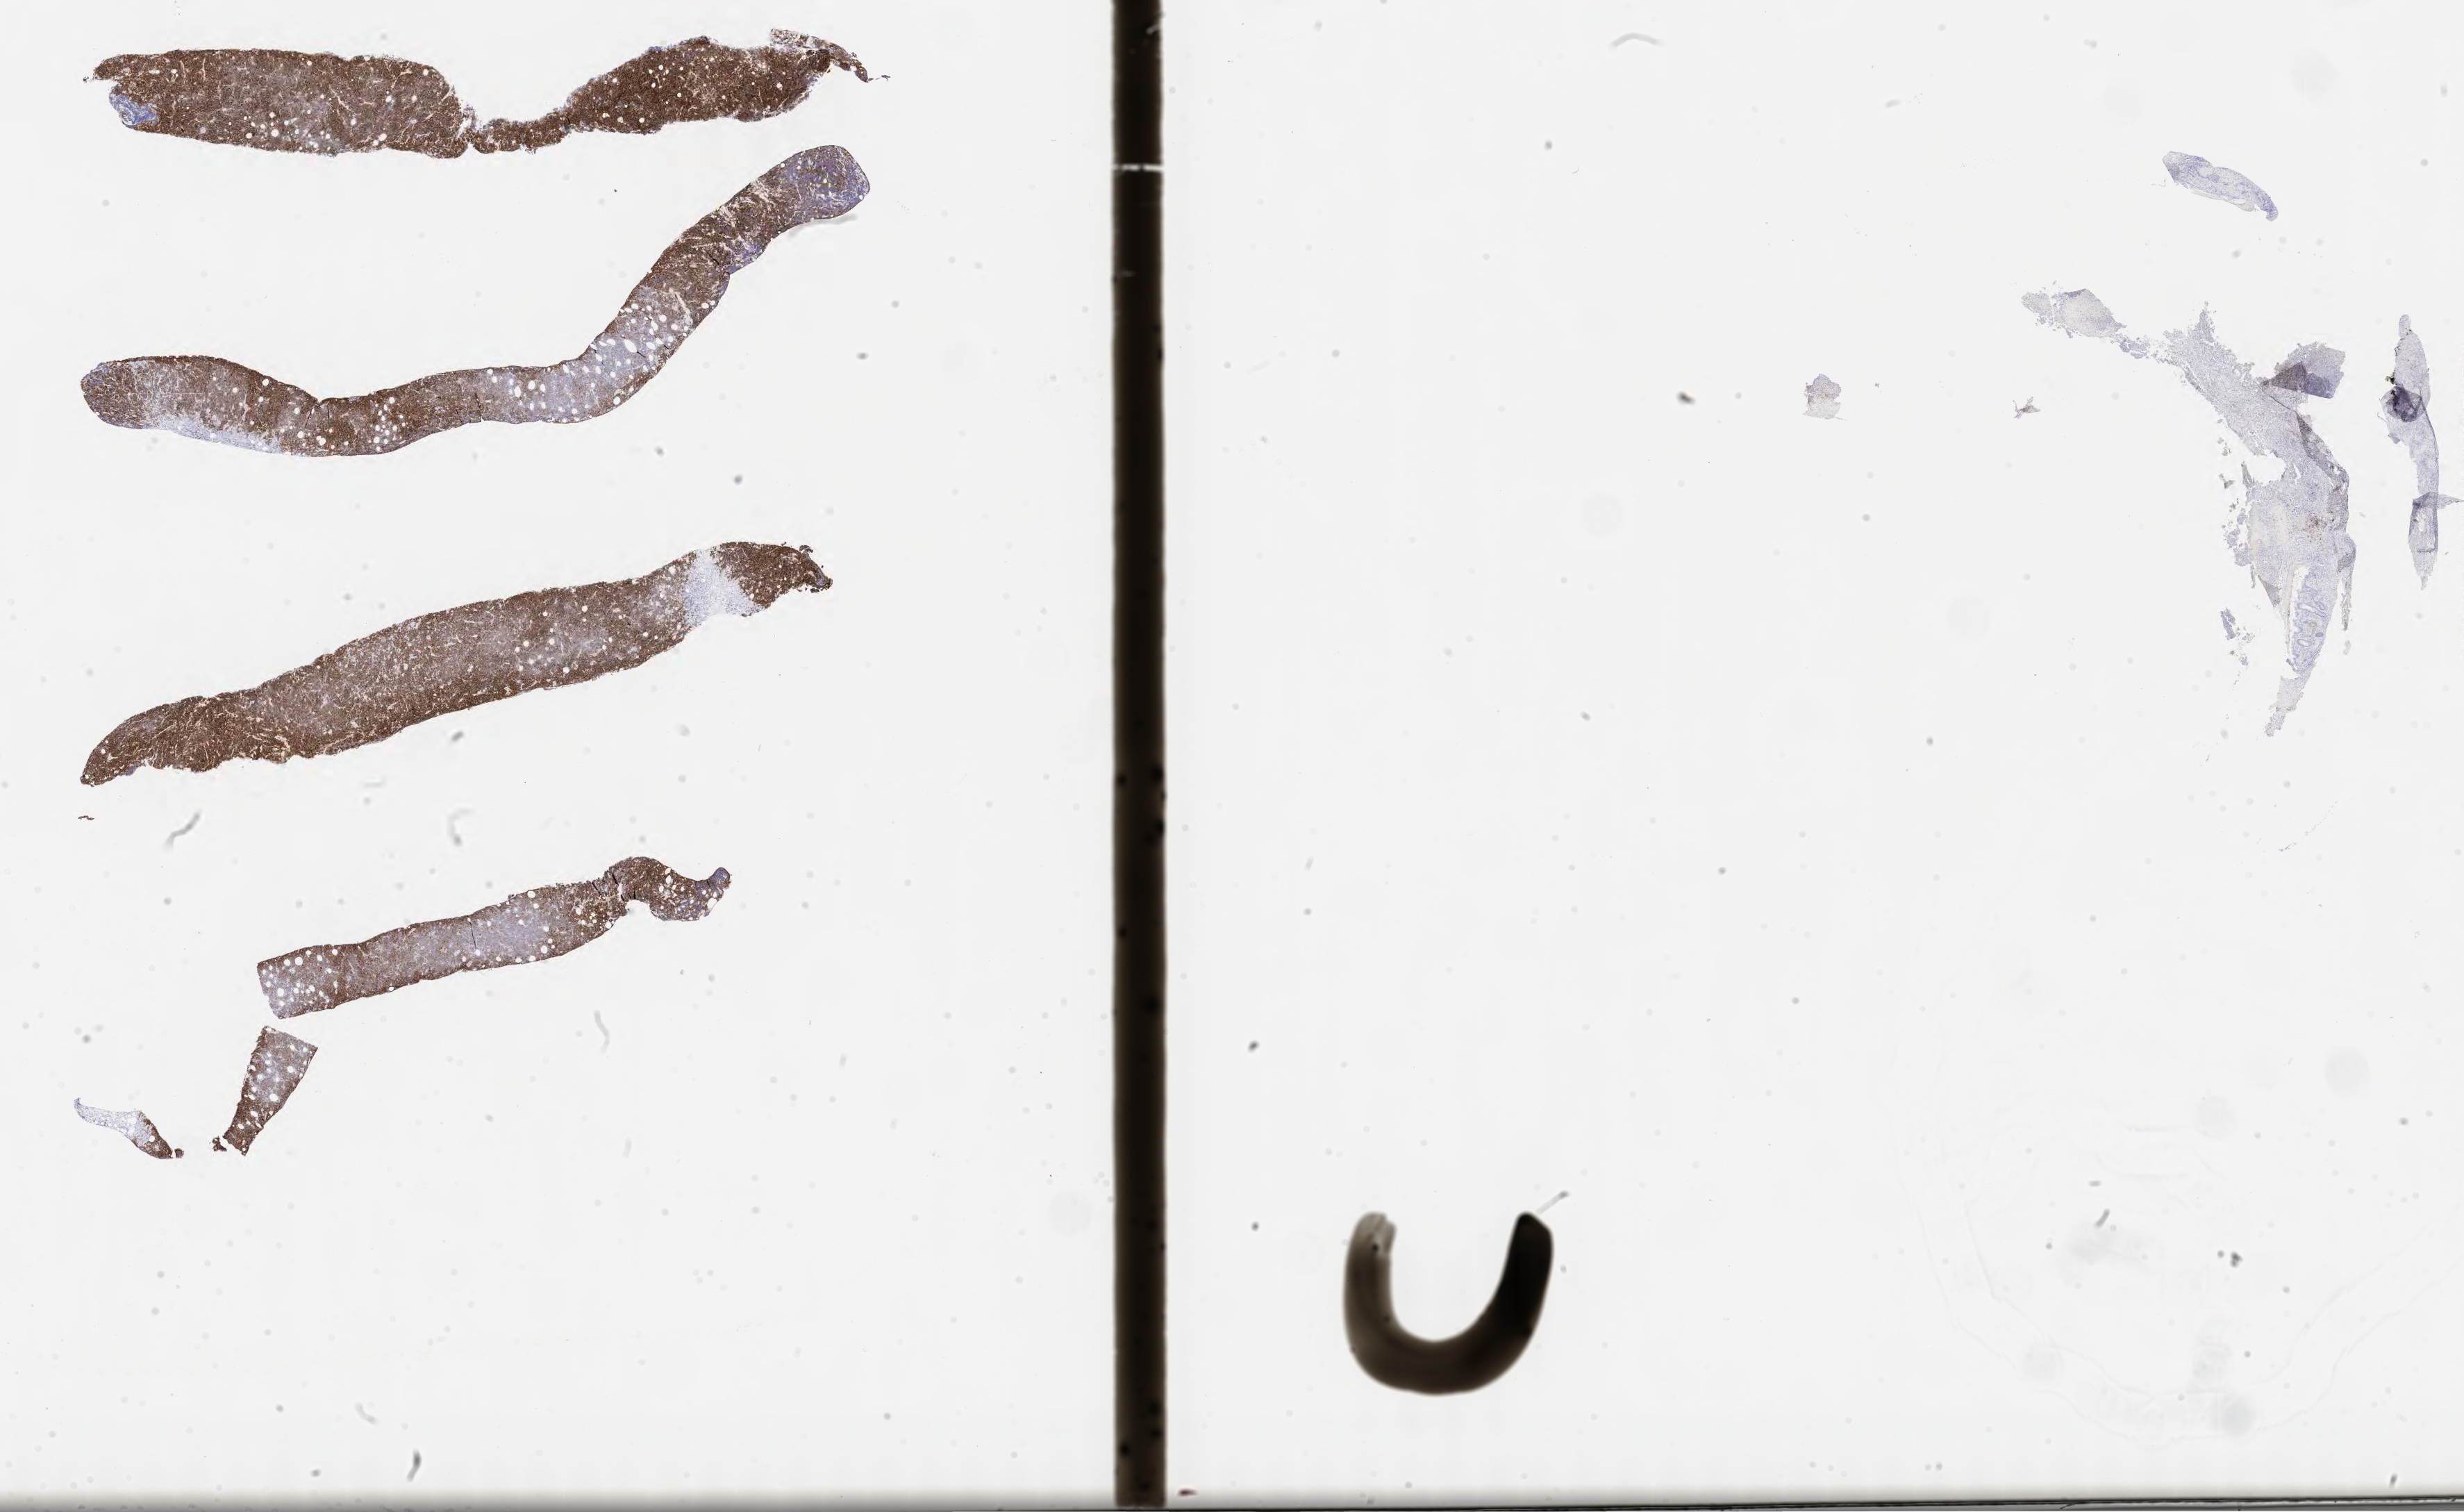
Whole-slide image, immunohistochemical stain for CD20 — whole scanned area (about 28.7 x 17.6 mm) shown as a low-resolution overview, specimen: tumor tissue. Male patient, 69 years old.
Diagnosis: Diffuse large B-cell lymphoma, NOS.